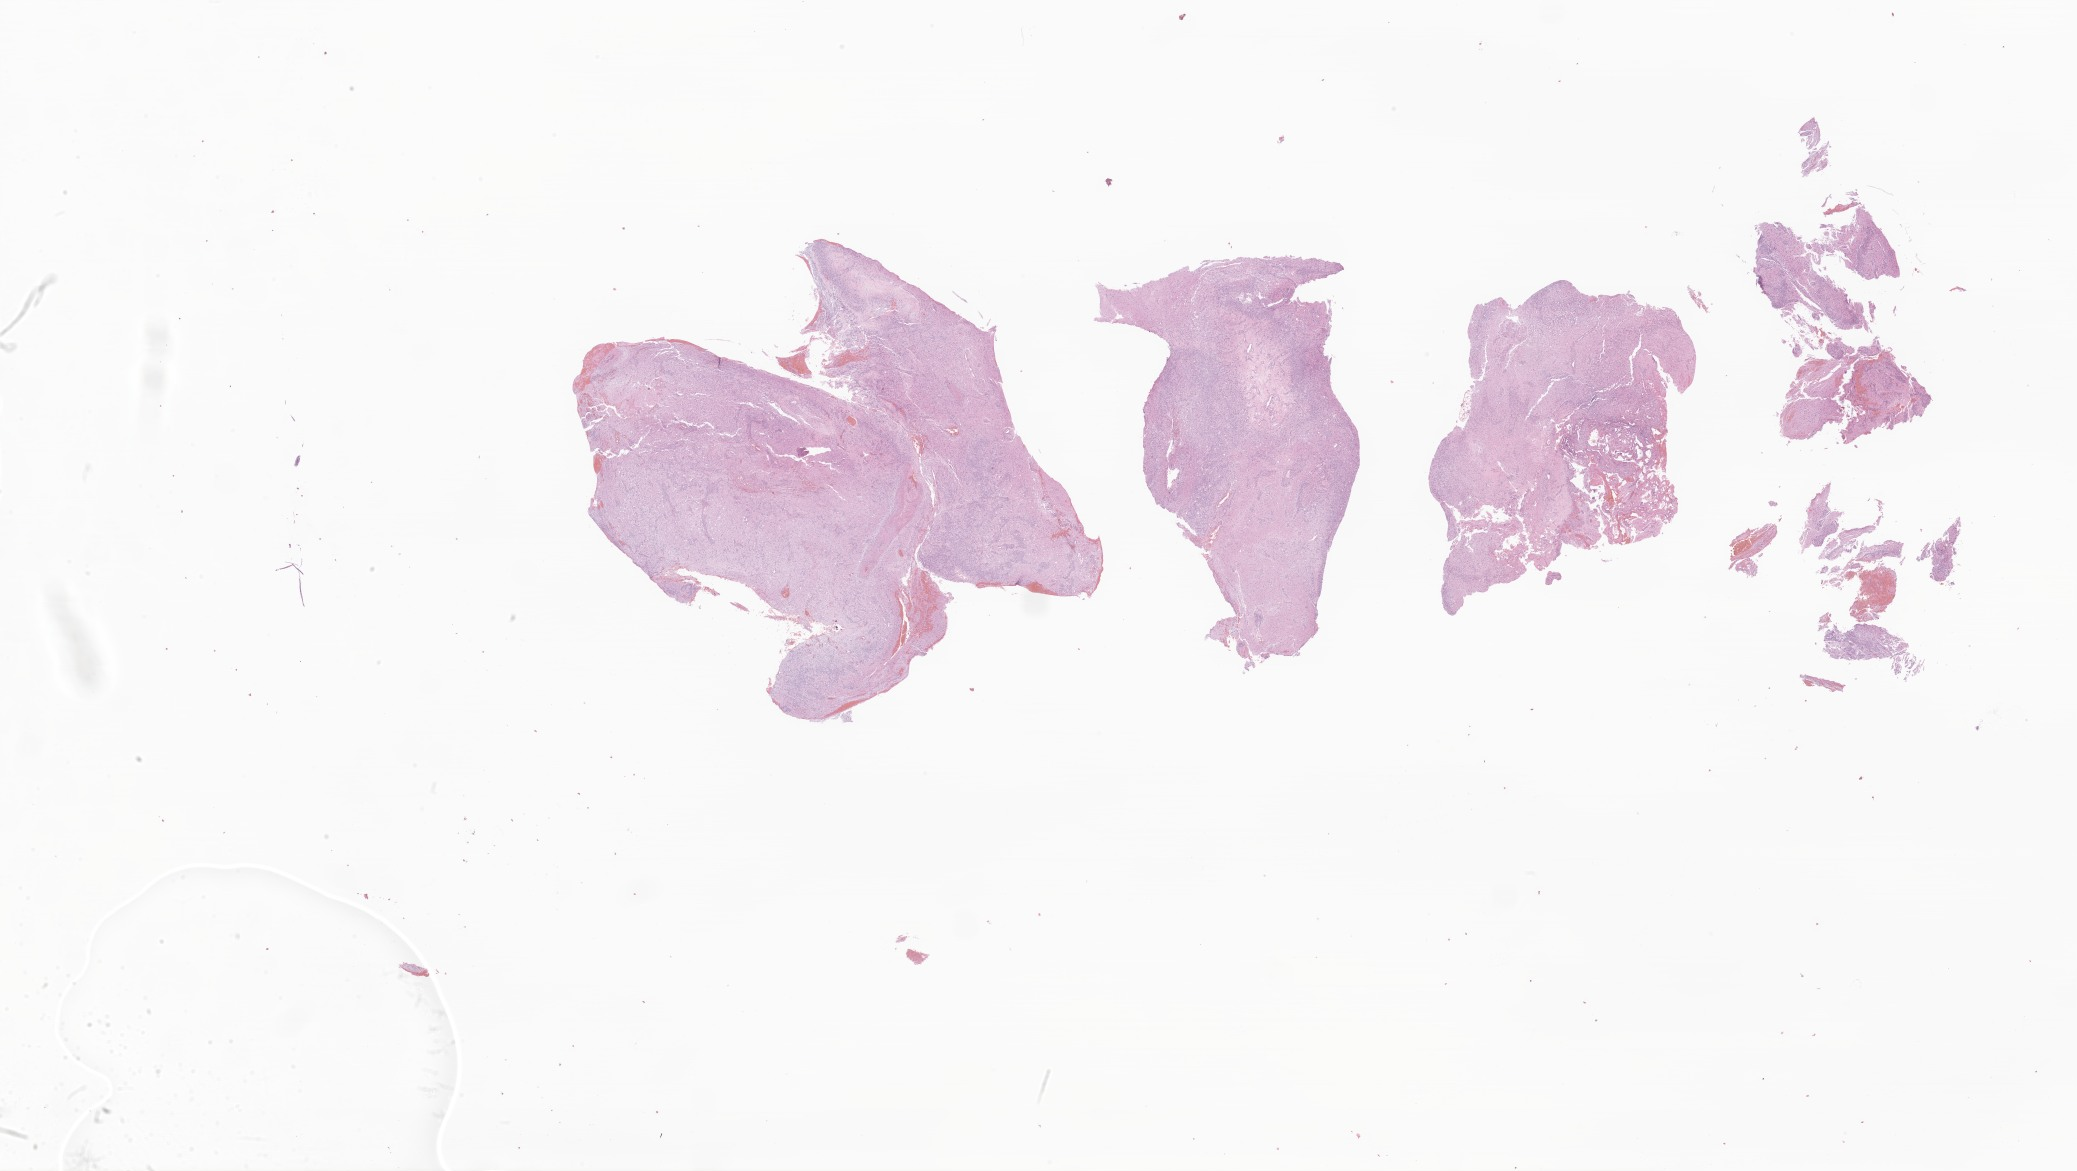
Digitized haematoxylin and eosin-stained section of tumor tissue from the brain — shown as a low-resolution overview of the whole scanned area (about 35.0 x 19.7 mm), formalin-fixed, paraffin-embedded (FFPE) tissue. Female patient, age 183 months (15 years 3 months).
• diagnosis (ICD-O-3 morphology term): Neoplasm, malignant